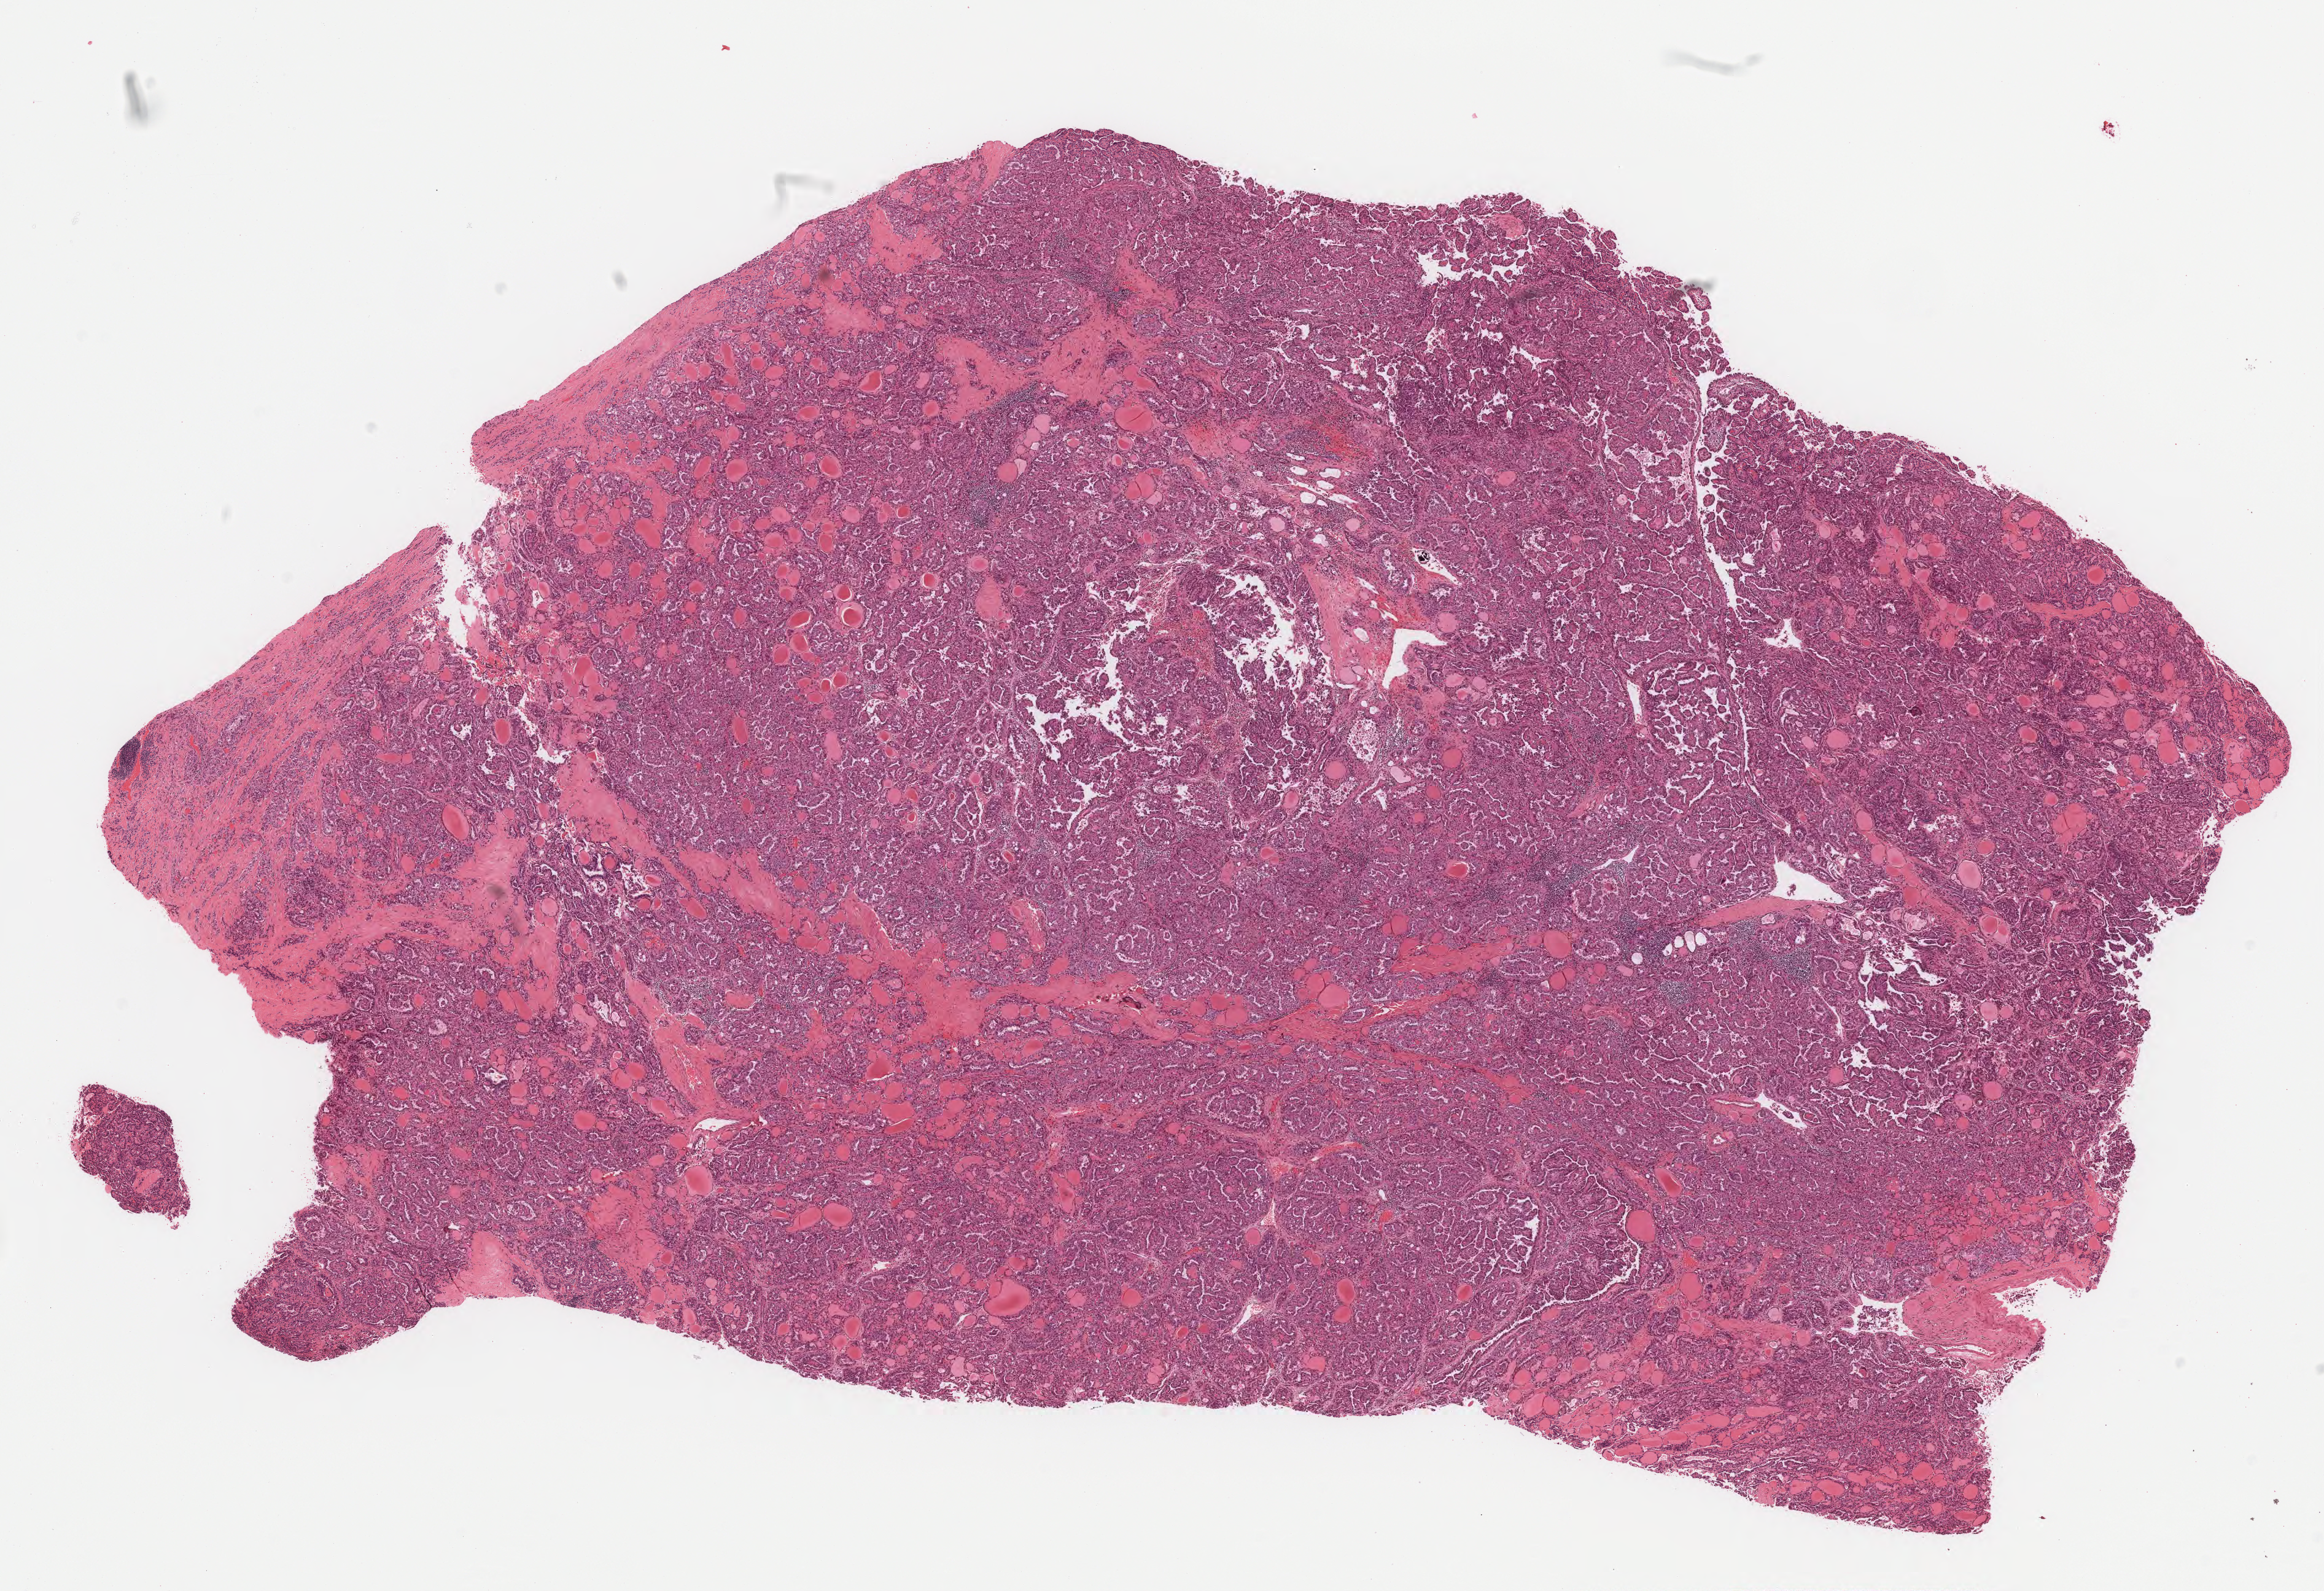
Digitized H&E-stained tissue section (whole slide) — low-resolution overview of the scanned area, about 15.2 x 10.4 mm (acquisition: 40x scan), formalin-fixed paraffin-embedded (FFPE) diagnostic section, thyroid, primary tumour sample. Male, age 61 years at initial diagnosis.
AJCC pathologic stage: IVA. Diagnosis: Papillary adenocarcinoma, NOS (thyroid gland). Lymph nodes positive (case pathology): 10 of 26 examined. Laterality: right.